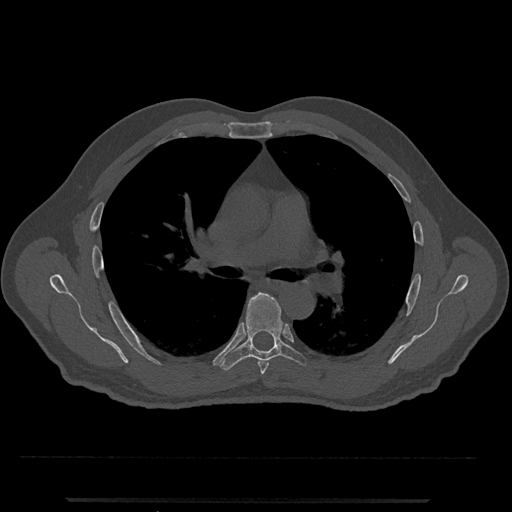
CT including the spine, one axial slice. Position 751 of 797 along the scan axis. Reconstruction kernel Br40s/3. 120 kVp. Bone window (W 1800 / L 400 HU). 0.5 mm slice thickness. 512 × 512 image matrix, field of view 419 × 419 mm. Male patient, age 63 years. Case-level facts recorded for this patient, not image findings: primary cancer: prostate.
Outlined on this slice (semi-automatic segmentation, software-assisted and operator-edited):
- T5 vertebra: bounding box <258,360,269,375> (left, top, right, bottom; pixels)
- T6 vertebra: <219,292,306,371>